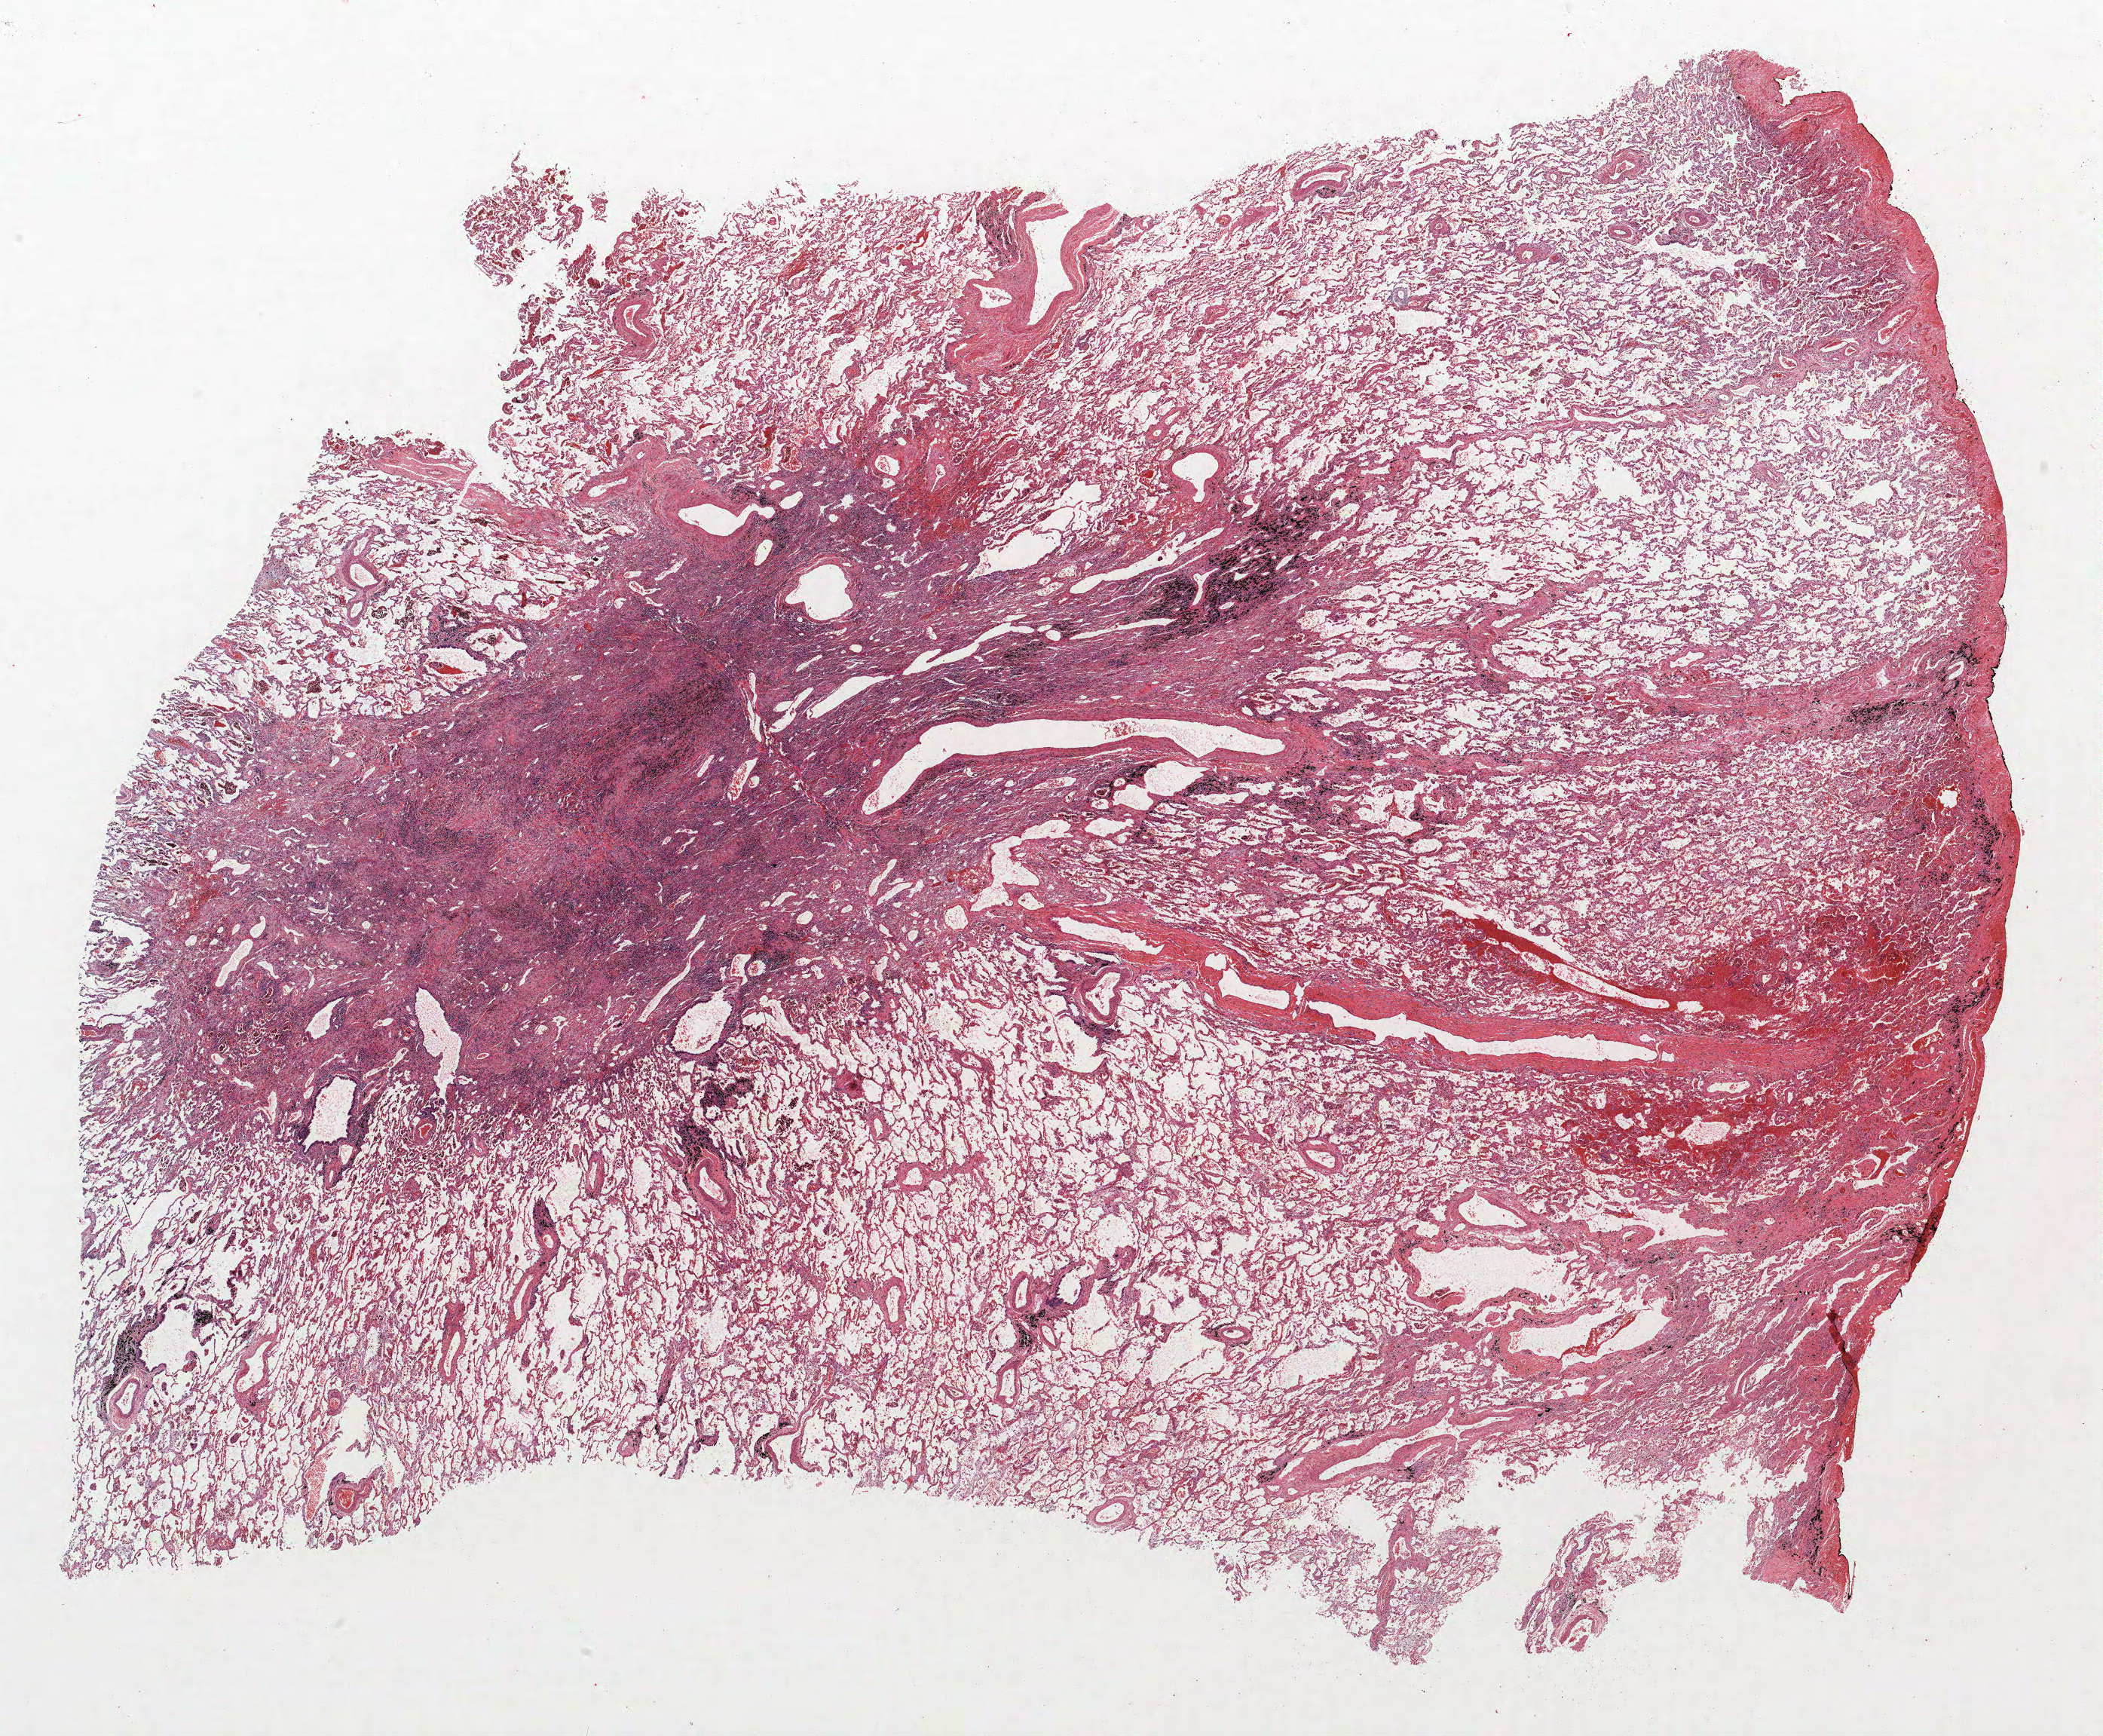
H&E whole-slide image, shown as a low-resolution overview of the whole scanned area (about 22.3 x 18.4 mm, slide scanned at 40x). FFPE section. Lung tissue. Male patient, aged 60 at enrolment. Former smoker at enrolment.
Participant's lung-cancer diagnosis: Adenocarcinoma, NOS (ICD-O-3 8140/3).